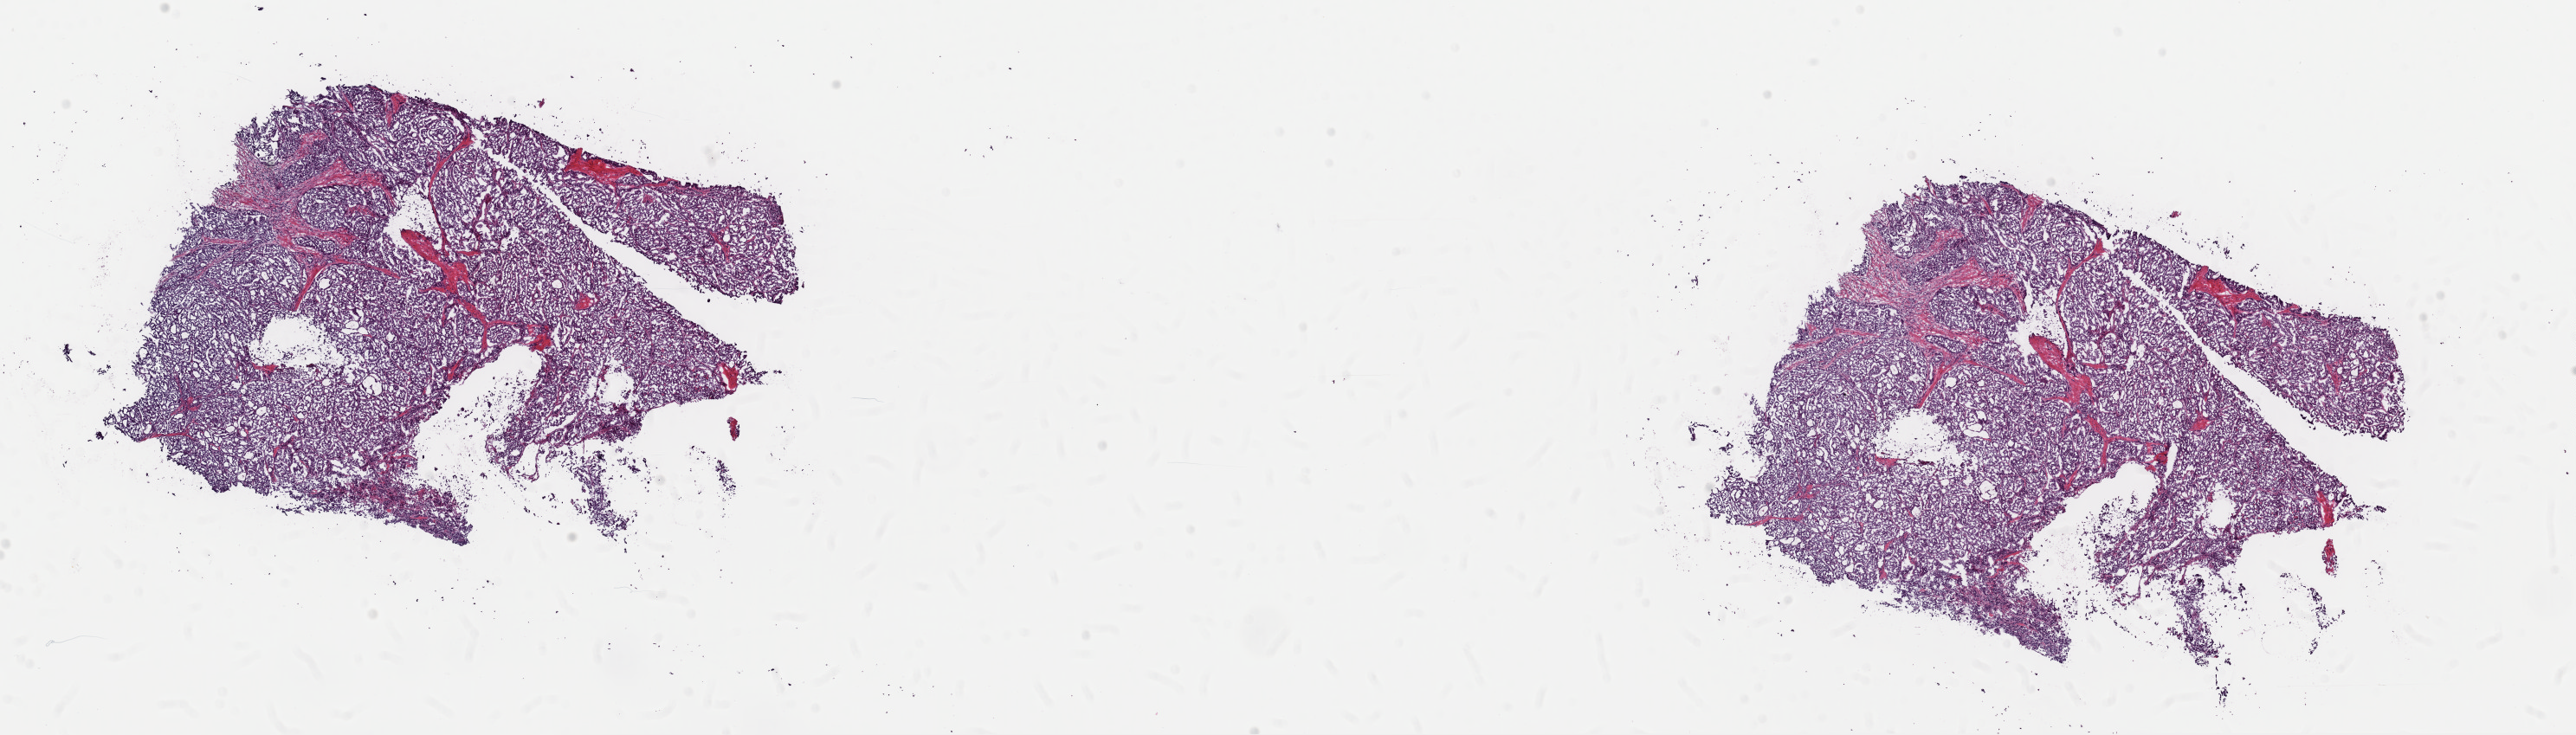
Digitized H&E tissue section (whole slide), low-resolution overview of the scanned area, about 23.5 x 6.7 mm (slide scanned at 40x), frozen section from the top of the tissue portion, sample: primary tumour, thyroid. Female, age 17 years at initial diagnosis. Pathologist review of this section (percent, as recorded): tumour cells 85%, tumour nuclei 100%.
Histologic diagnosis: Papillary carcinoma, follicular variant (thyroid gland).